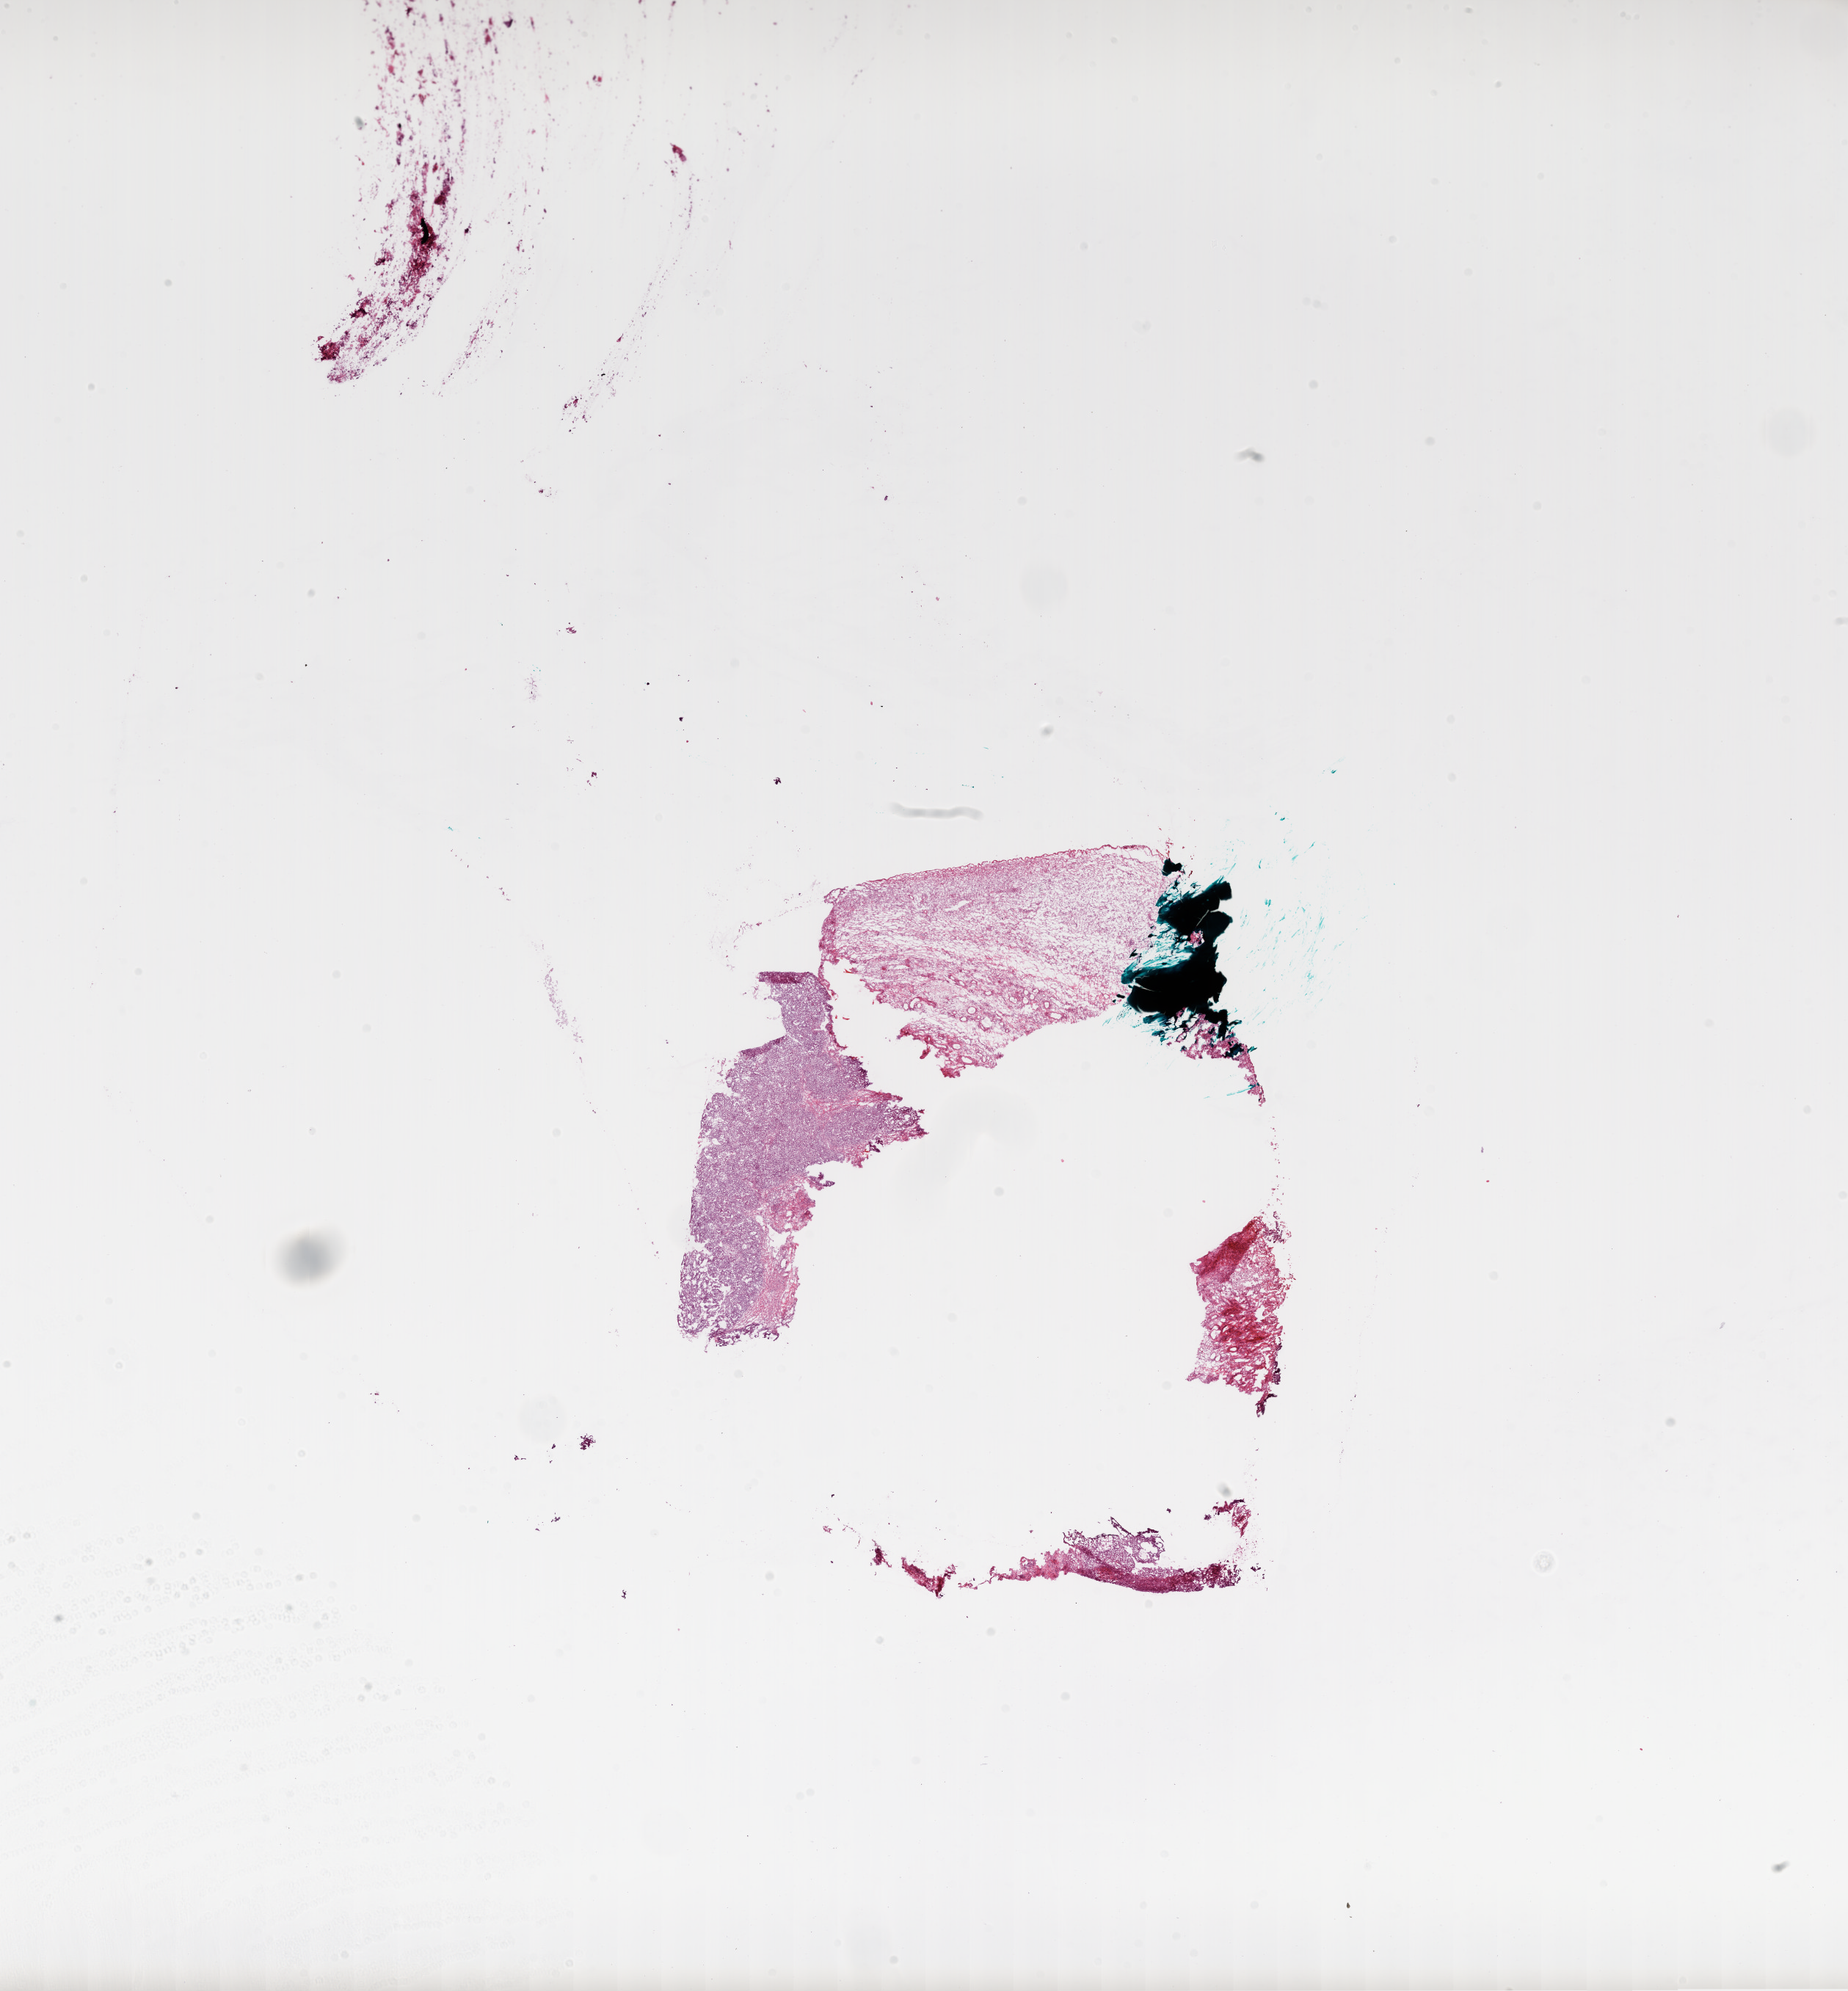
Digitized H&E tissue section (whole slide), a low-resolution overview of the entire scanned area, about 20.3 x 21.9 mm (from a 20x scan). Frozen section. Sample: primary tumour, ovary. Female patient; age at initial diagnosis 65 years. Histologic grade: G3 (poorly differentiated). Composition of this section per pathologist review: tumour cells 70%, tumour nuclei 70%, normal cells 20%, stromal cells 10%, necrosis 0%.
Laterality: right. FIGO stage: IIIC. Pathologic diagnosis: Serous cystadenocarcinoma, NOS.